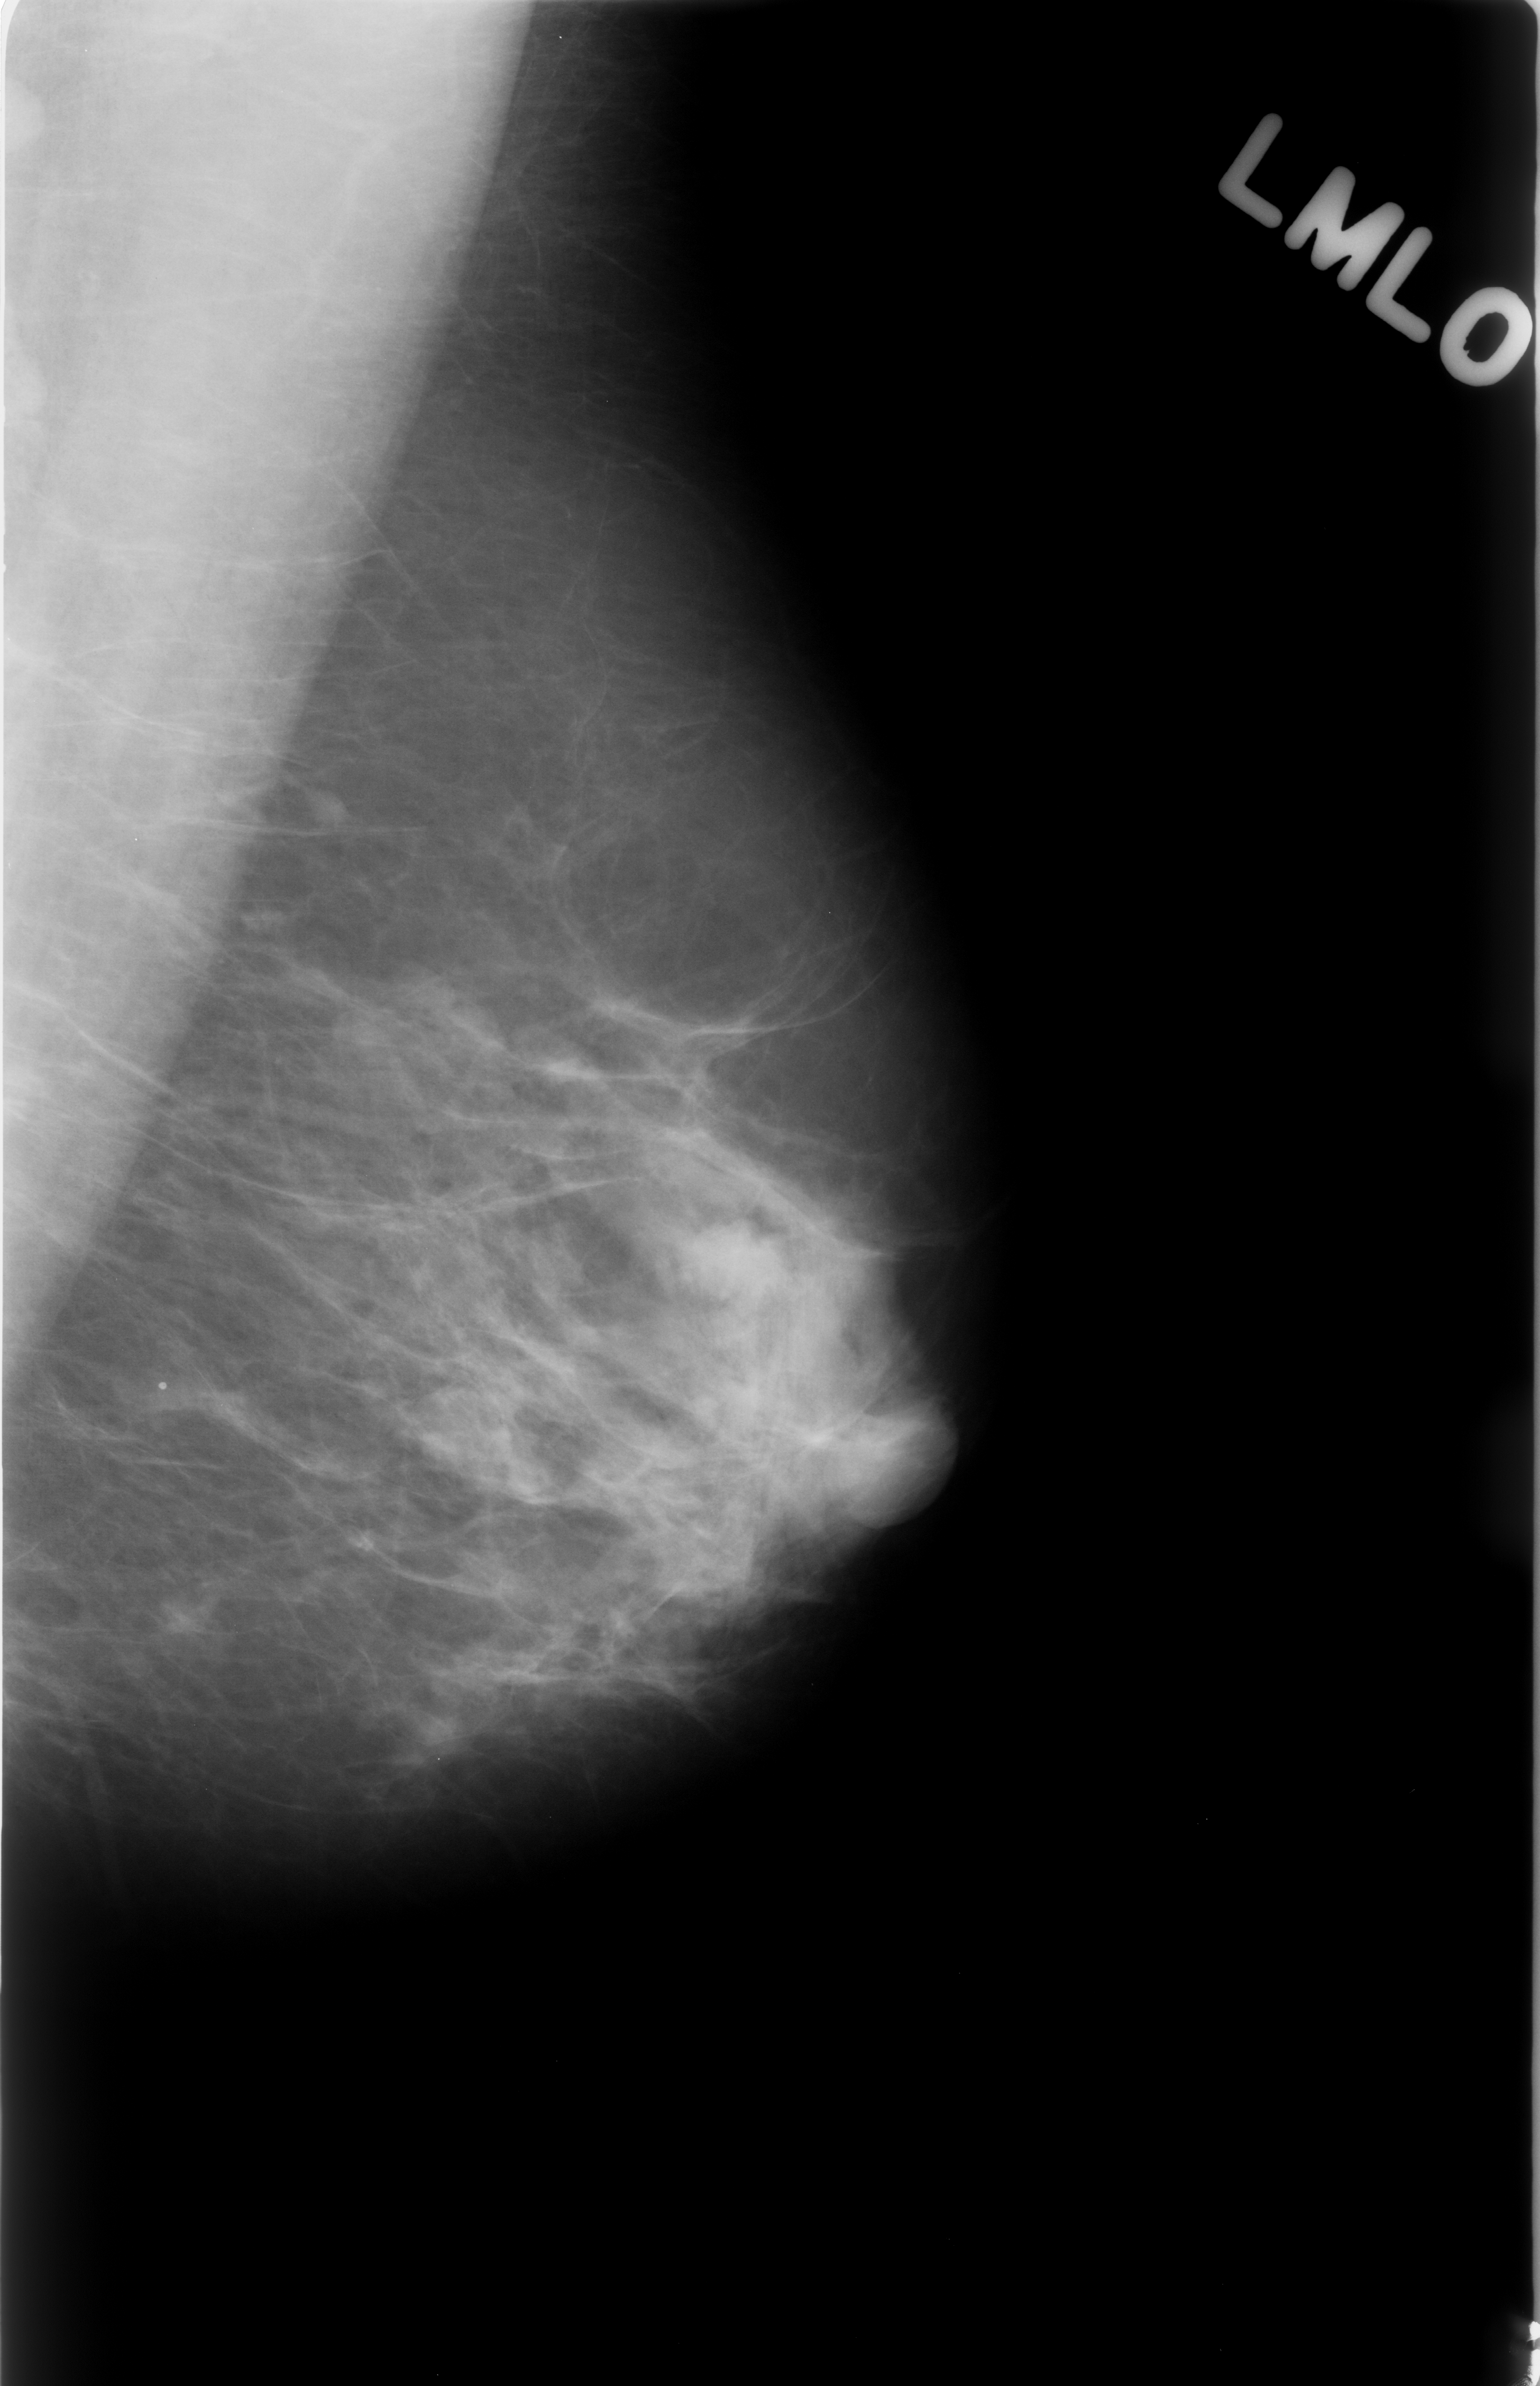
Scanned film-screen mammogram; left breast; MLO view; BI-RADS breast density category 2 (scale 1–4); 1540 × 2386 image matrix.
Expert-marked regions of interest on this image (one box per marked abnormality):
- mass, shape lobulated, margins circumscribed; BI-RADS assessment category 4; subtlety rating 5 on a 1 (subtle) to 5 (obvious) scale; pathology (as recorded): benign: bounding box (x1, y1, x2, y2) in pixels: (667, 1220, 788, 1300)